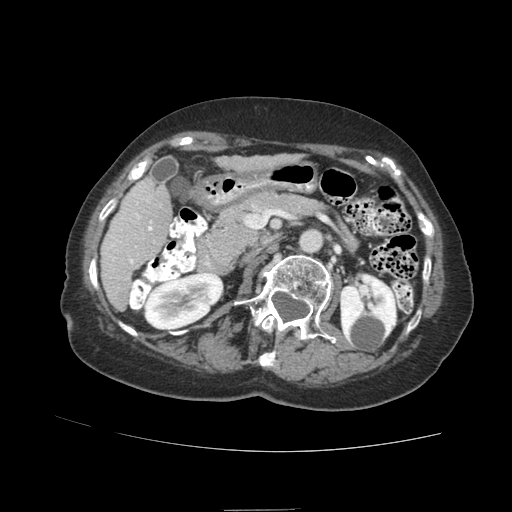
Contrast-enhanced abdominal CT (liver protocol), one axial slice. Slice 31 of 89 in the series (ordered by position). Reconstruction kernel STANDARD. 140 kVp. Soft-tissue window (W 400 / L 40 HU). 2.5 mm slice thickness. 512 × 512 image matrix, field of view 360 × 360 mm. Case-level facts recorded for this patient, not image findings: diagnosis: hepatocellular carcinoma (patient treated with transarterial chemoembolisation; whether this scan precedes or follows treatment is not stated here); TNM stage (as recorded): Stage-II; Child-Pugh class: A; tumour differentiation: moderately differentiated; tumour size: 4 cm.
Annotated regions visible in this slice (semi-automatic segmentation, software-assisted and operator-edited):
- liver parenchyma outside the tumour (the mass and vessels are separate outlines, so this box may not span the whole liver): bounding box (x1, y1, x2, y2) in pixels: (100, 176, 172, 310)
- liver vessels: (110, 200, 153, 264)